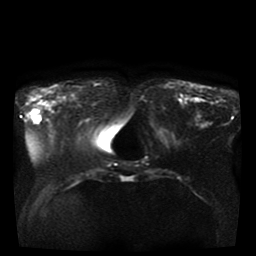
Breast MRI, one axial slice. Diffusion-weighted series; image 2 of 4 stored at this slice position (different b-values; order by instance number). 1.5 T. 256 × 256 image matrix. Female patient.
Annotated regions visible in this slice (expert manual segmentation):
- tumour on diffusion-weighted imaging: bounding box [x1, y1, x2, y2] px = [33, 109, 41, 124]